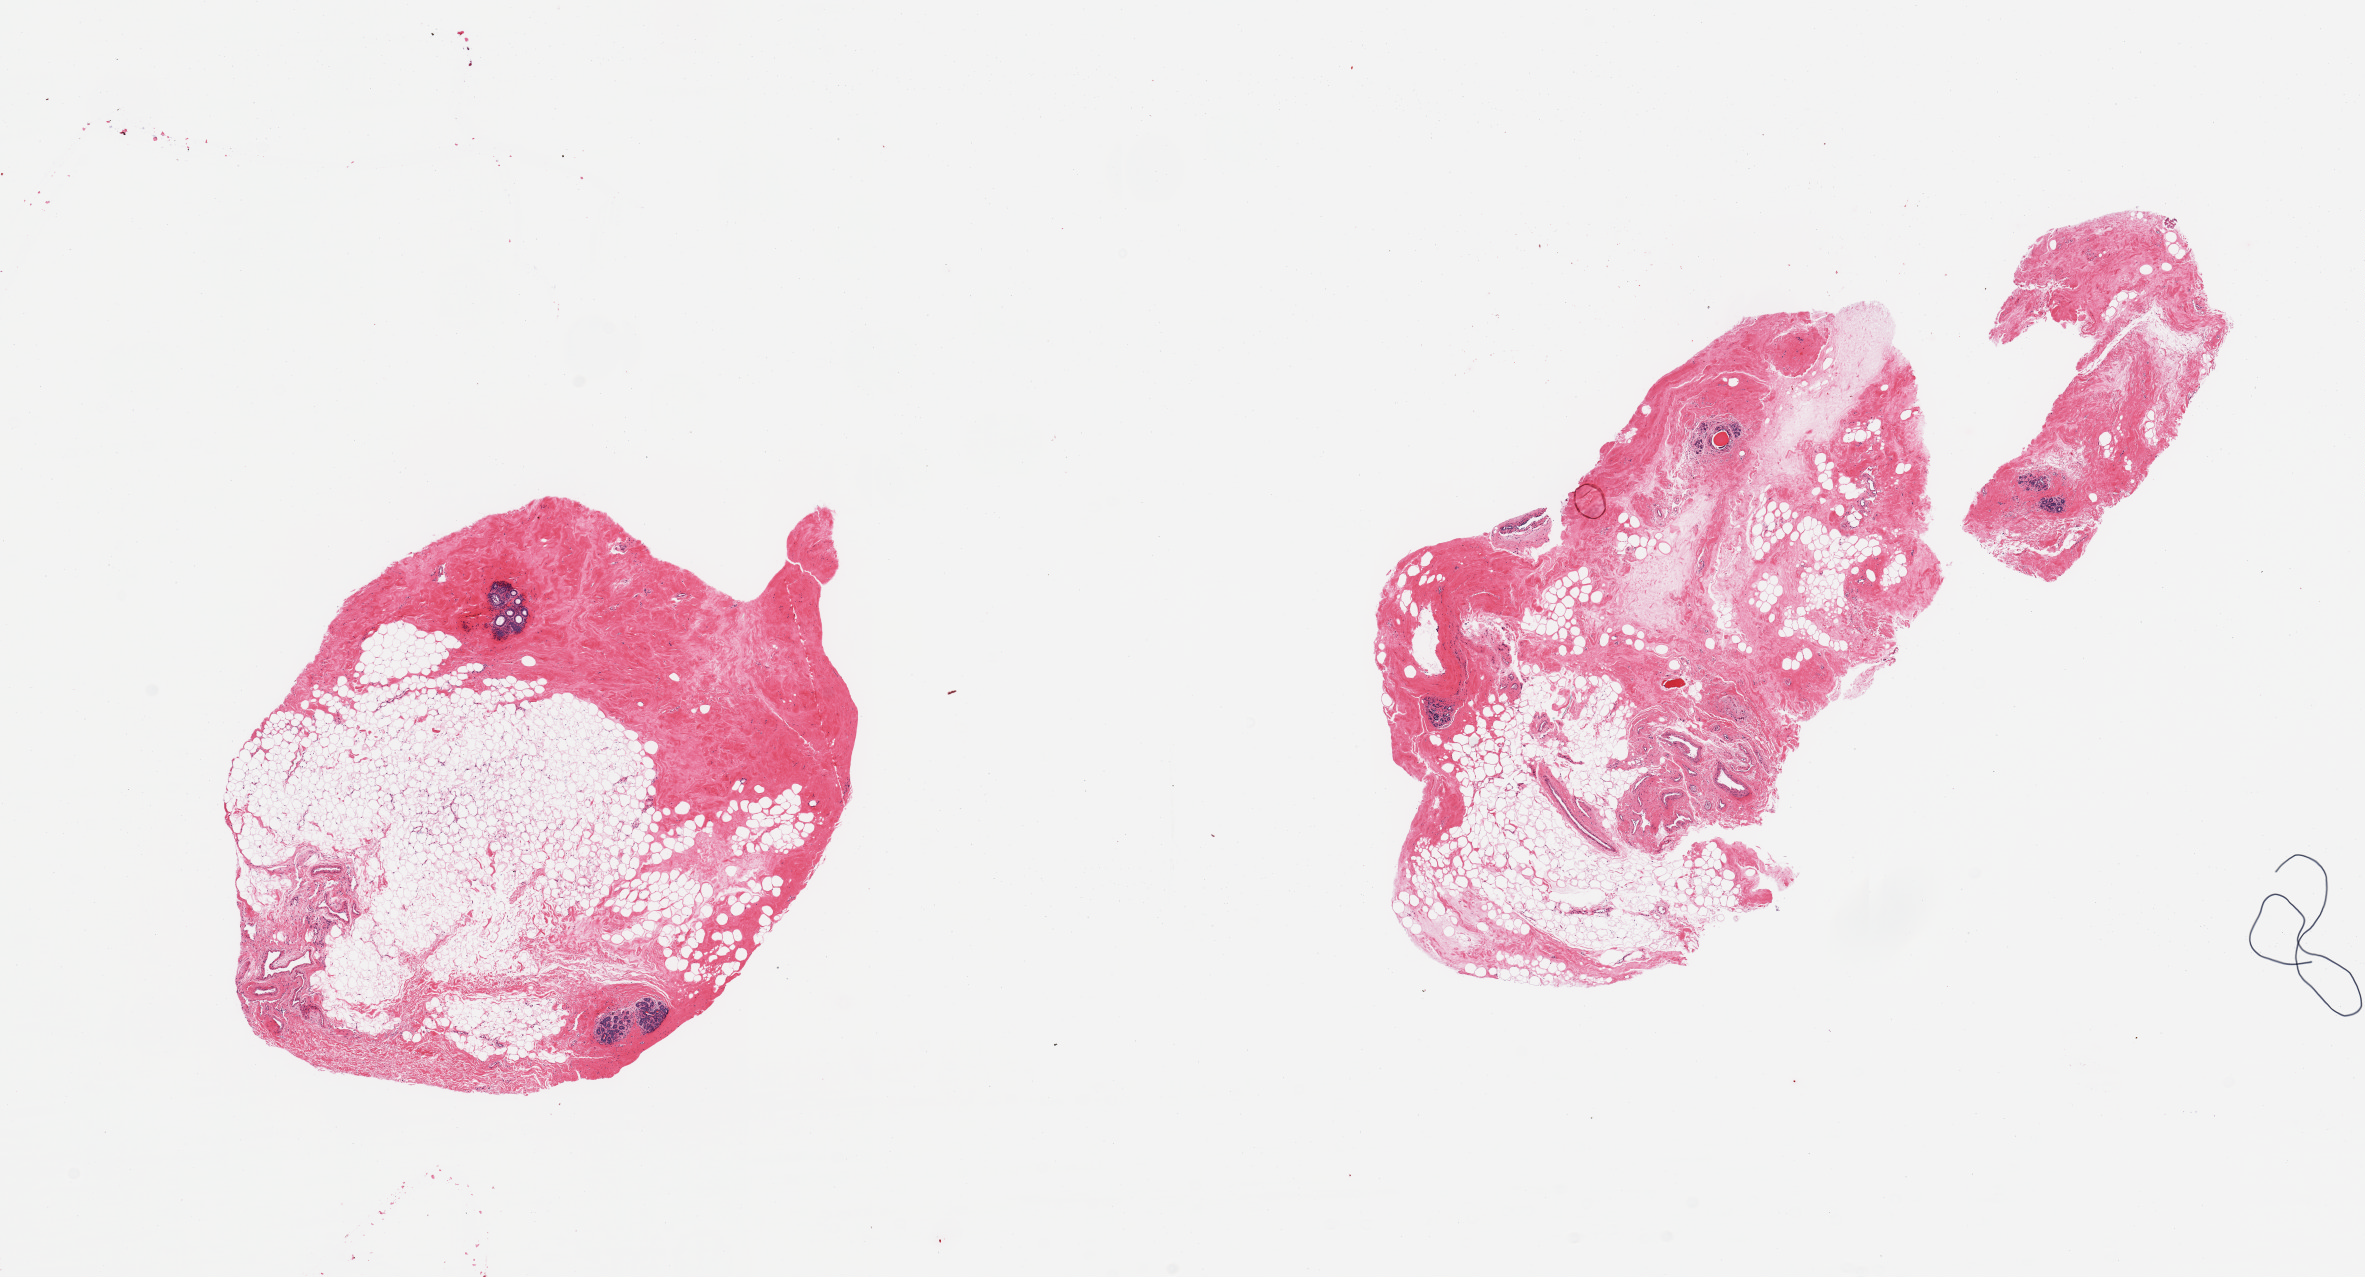
Digitized H&E-stained section, whole scanned area (about 18.7 x 10.1 mm, slide scanned at 20x) shown as a low-resolution overview. PAXgene-fixed, paraffin-embedded tissue. Section of breast (target tissue). Tissue donor sample. Donor: female.
Reviewer comment on this tissue sample: 2 pieces; mainly fibroadipose elements; few TDLUs.